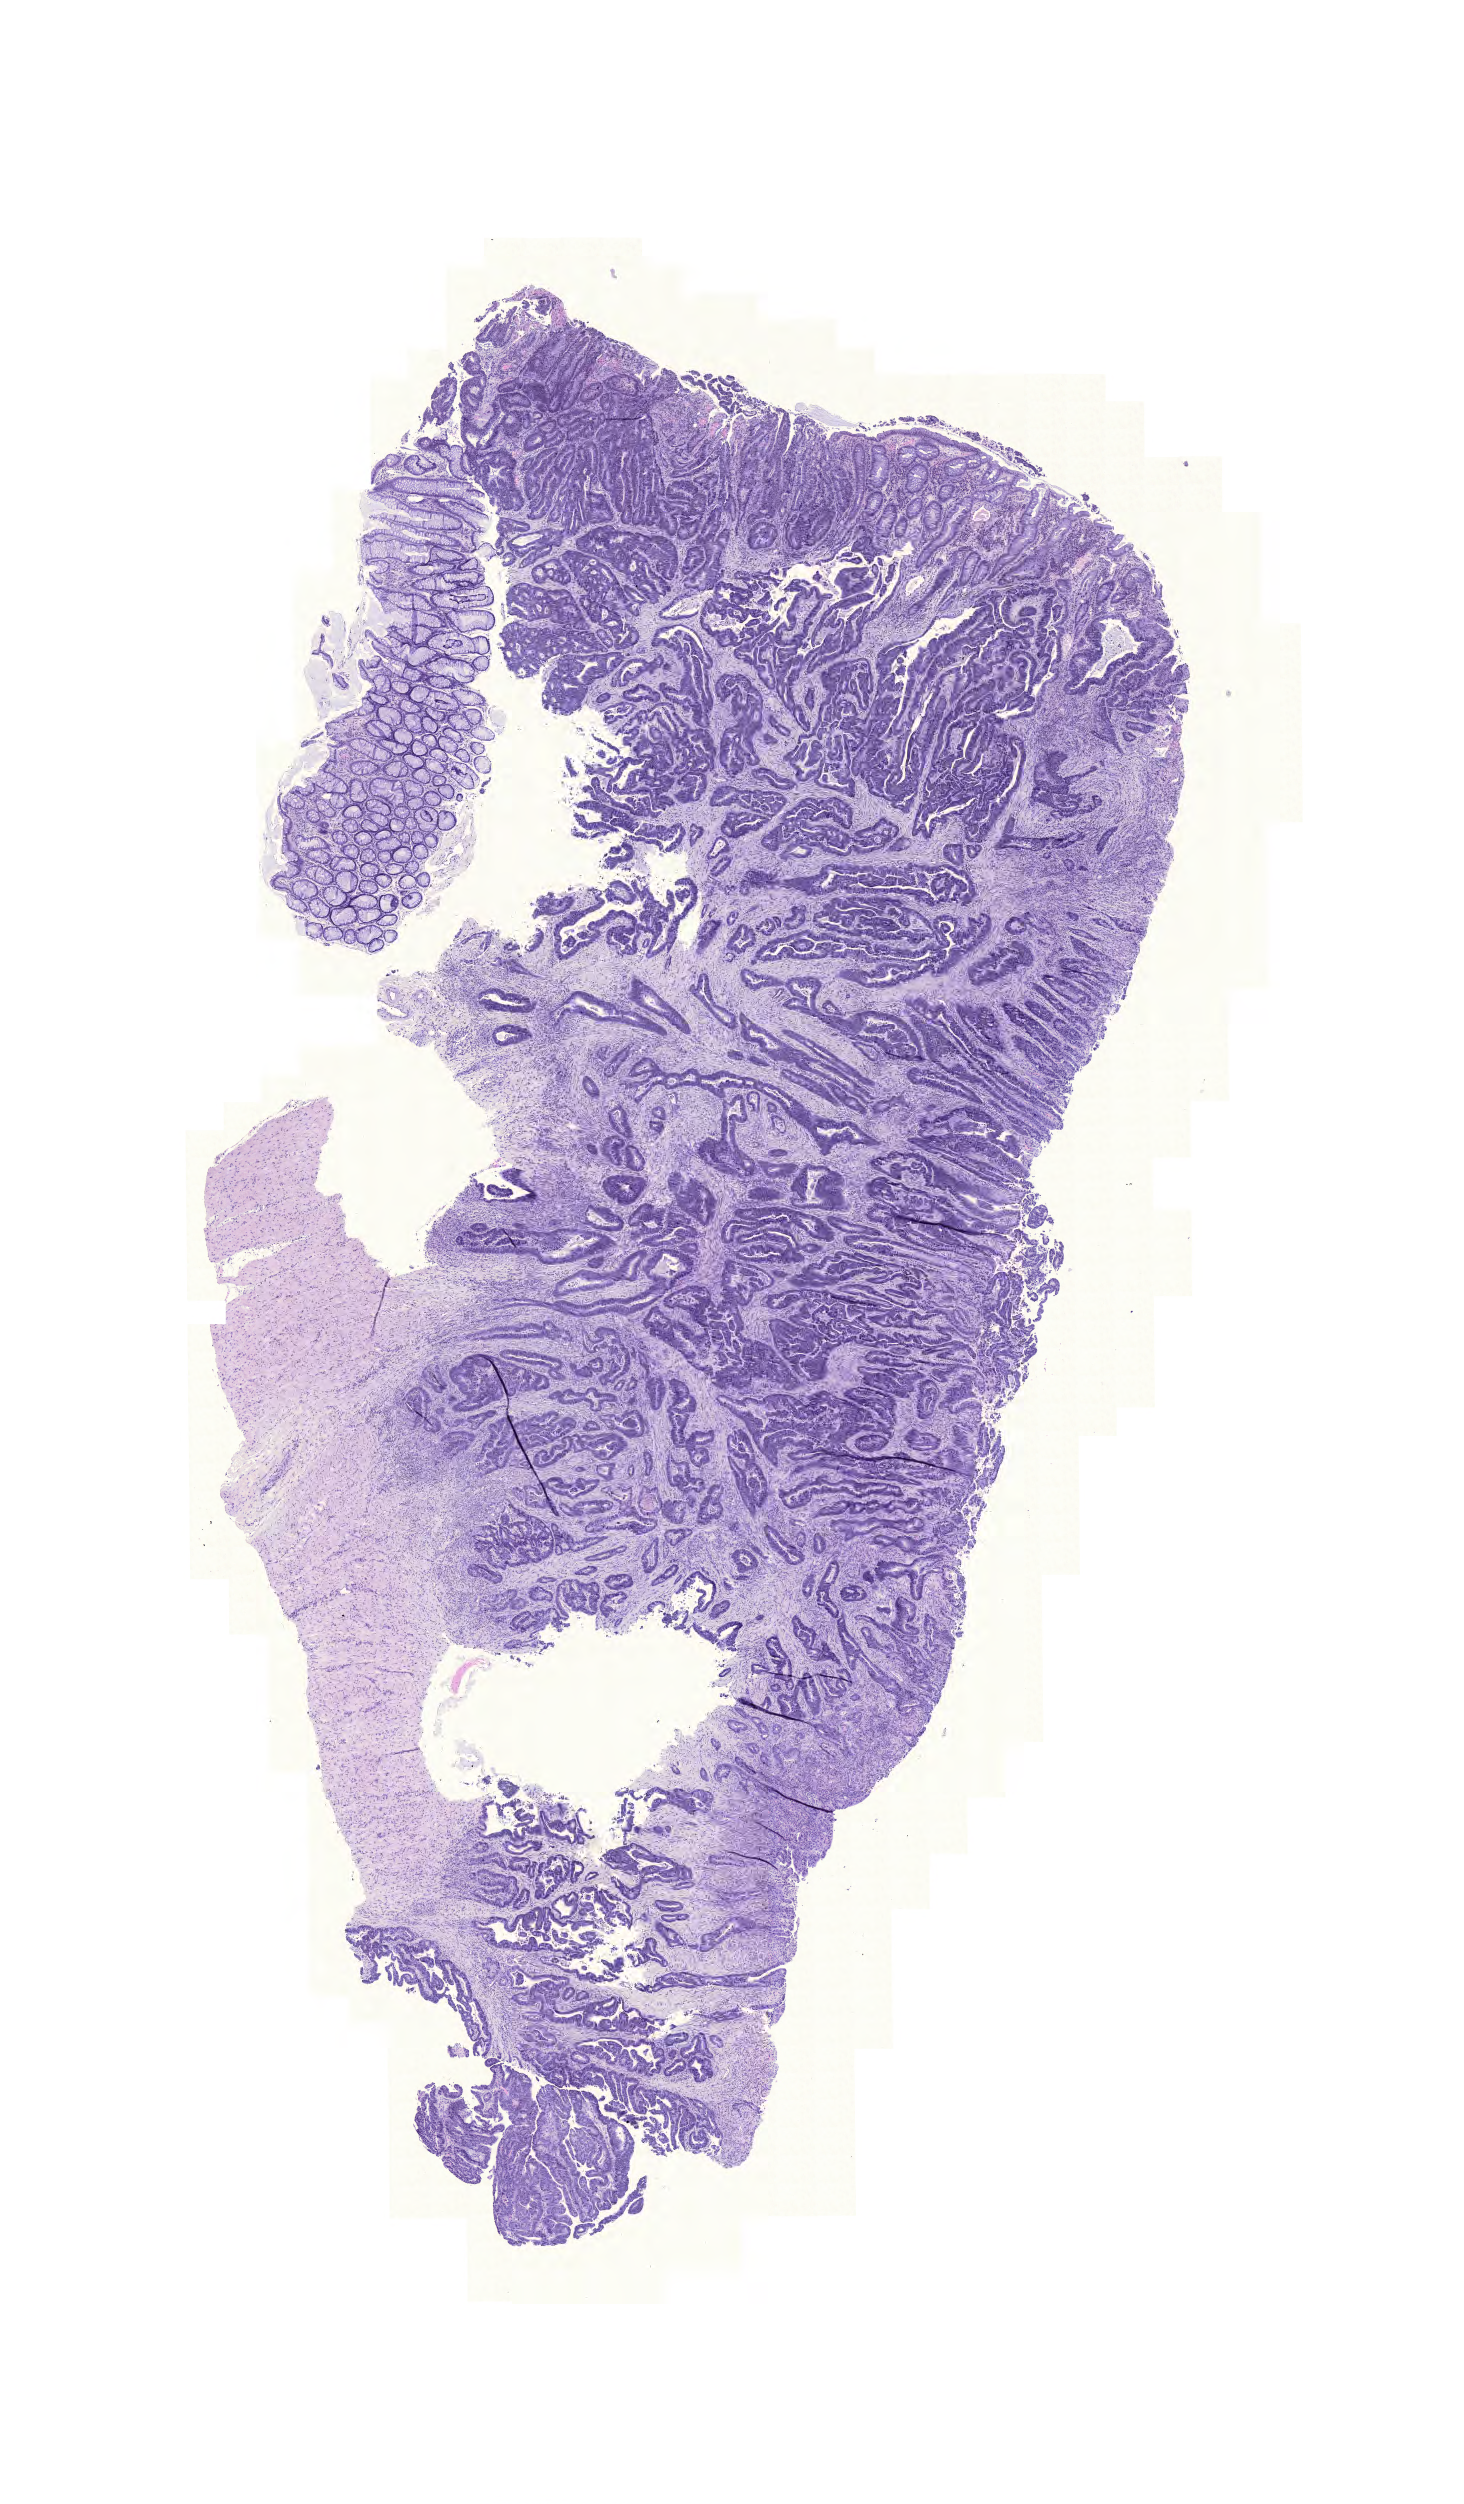
Whole-slide histology image, Hematoxylin and eosin (H&E) stained — whole scanned area (about 10.9 x 18.6 mm, from a 20x scan) shown as a low-resolution overview, formalin-fixed paraffin-embedded (FFPE) diagnostic section, colon, primary tumour sample. Patient: male, age at initial diagnosis 80 years.
* diagnosis: Adenocarcinoma, NOS
* AJCC pathologic stage: I (6th edition)
* lymph nodes positive (case pathology): 0 of 14 examined